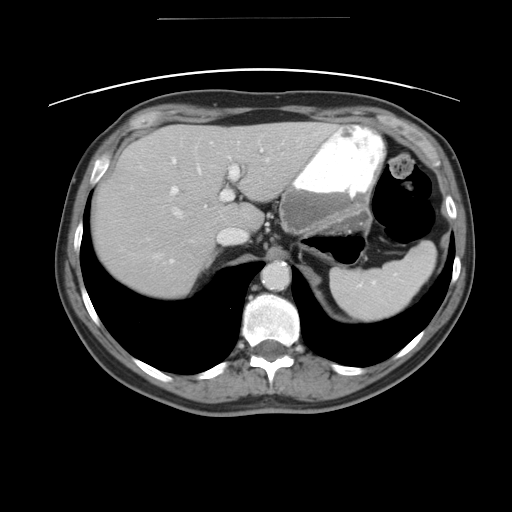
Contrast-enhanced abdominal CT, one axial slice; position 34 of 49 along the scan axis; intravenous contrast given; soft-tissue window (W 400 / L 40 HU); 5 mm slice thickness; 512 × 512 image matrix. Male patient, age 57 years. Case-level facts recorded for this patient, not image findings: diagnosis: colorectal cancer liver metastases, imaged before liver resection.
Annotated regions visible in this slice (outlined manually by an expert reader):
- hepatic veins: bounding box <154,157,267,256> (left, top, right, bottom; pixels)
- liver: <92,121,336,298>
- planned liver remnant (the part of the liver to remain after resection): <208,122,336,231>
- portal vein (with intrahepatic branches): <169,140,263,206>